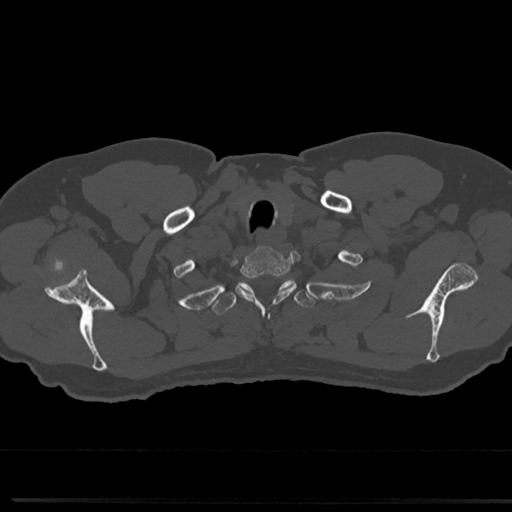
CT including the spine, one axial slice; position 657 of 817 along the scan axis; reconstruction kernel Br40s/3; bone window (W 1800 / L 400 HU); 0.5 mm slice thickness; 512 × 512 image matrix, field of view 355 × 355 mm. Patient: male, 61 years. From the clinical record (not read from this slice): primary cancer: prostate.
Structures marked on this image (semi-automatically segmented with operator editing):
- T1 vertebra: bounding box <238,249,288,300> (left, top, right, bottom; pixels)
- T2 vertebra: <216,276,311,313>